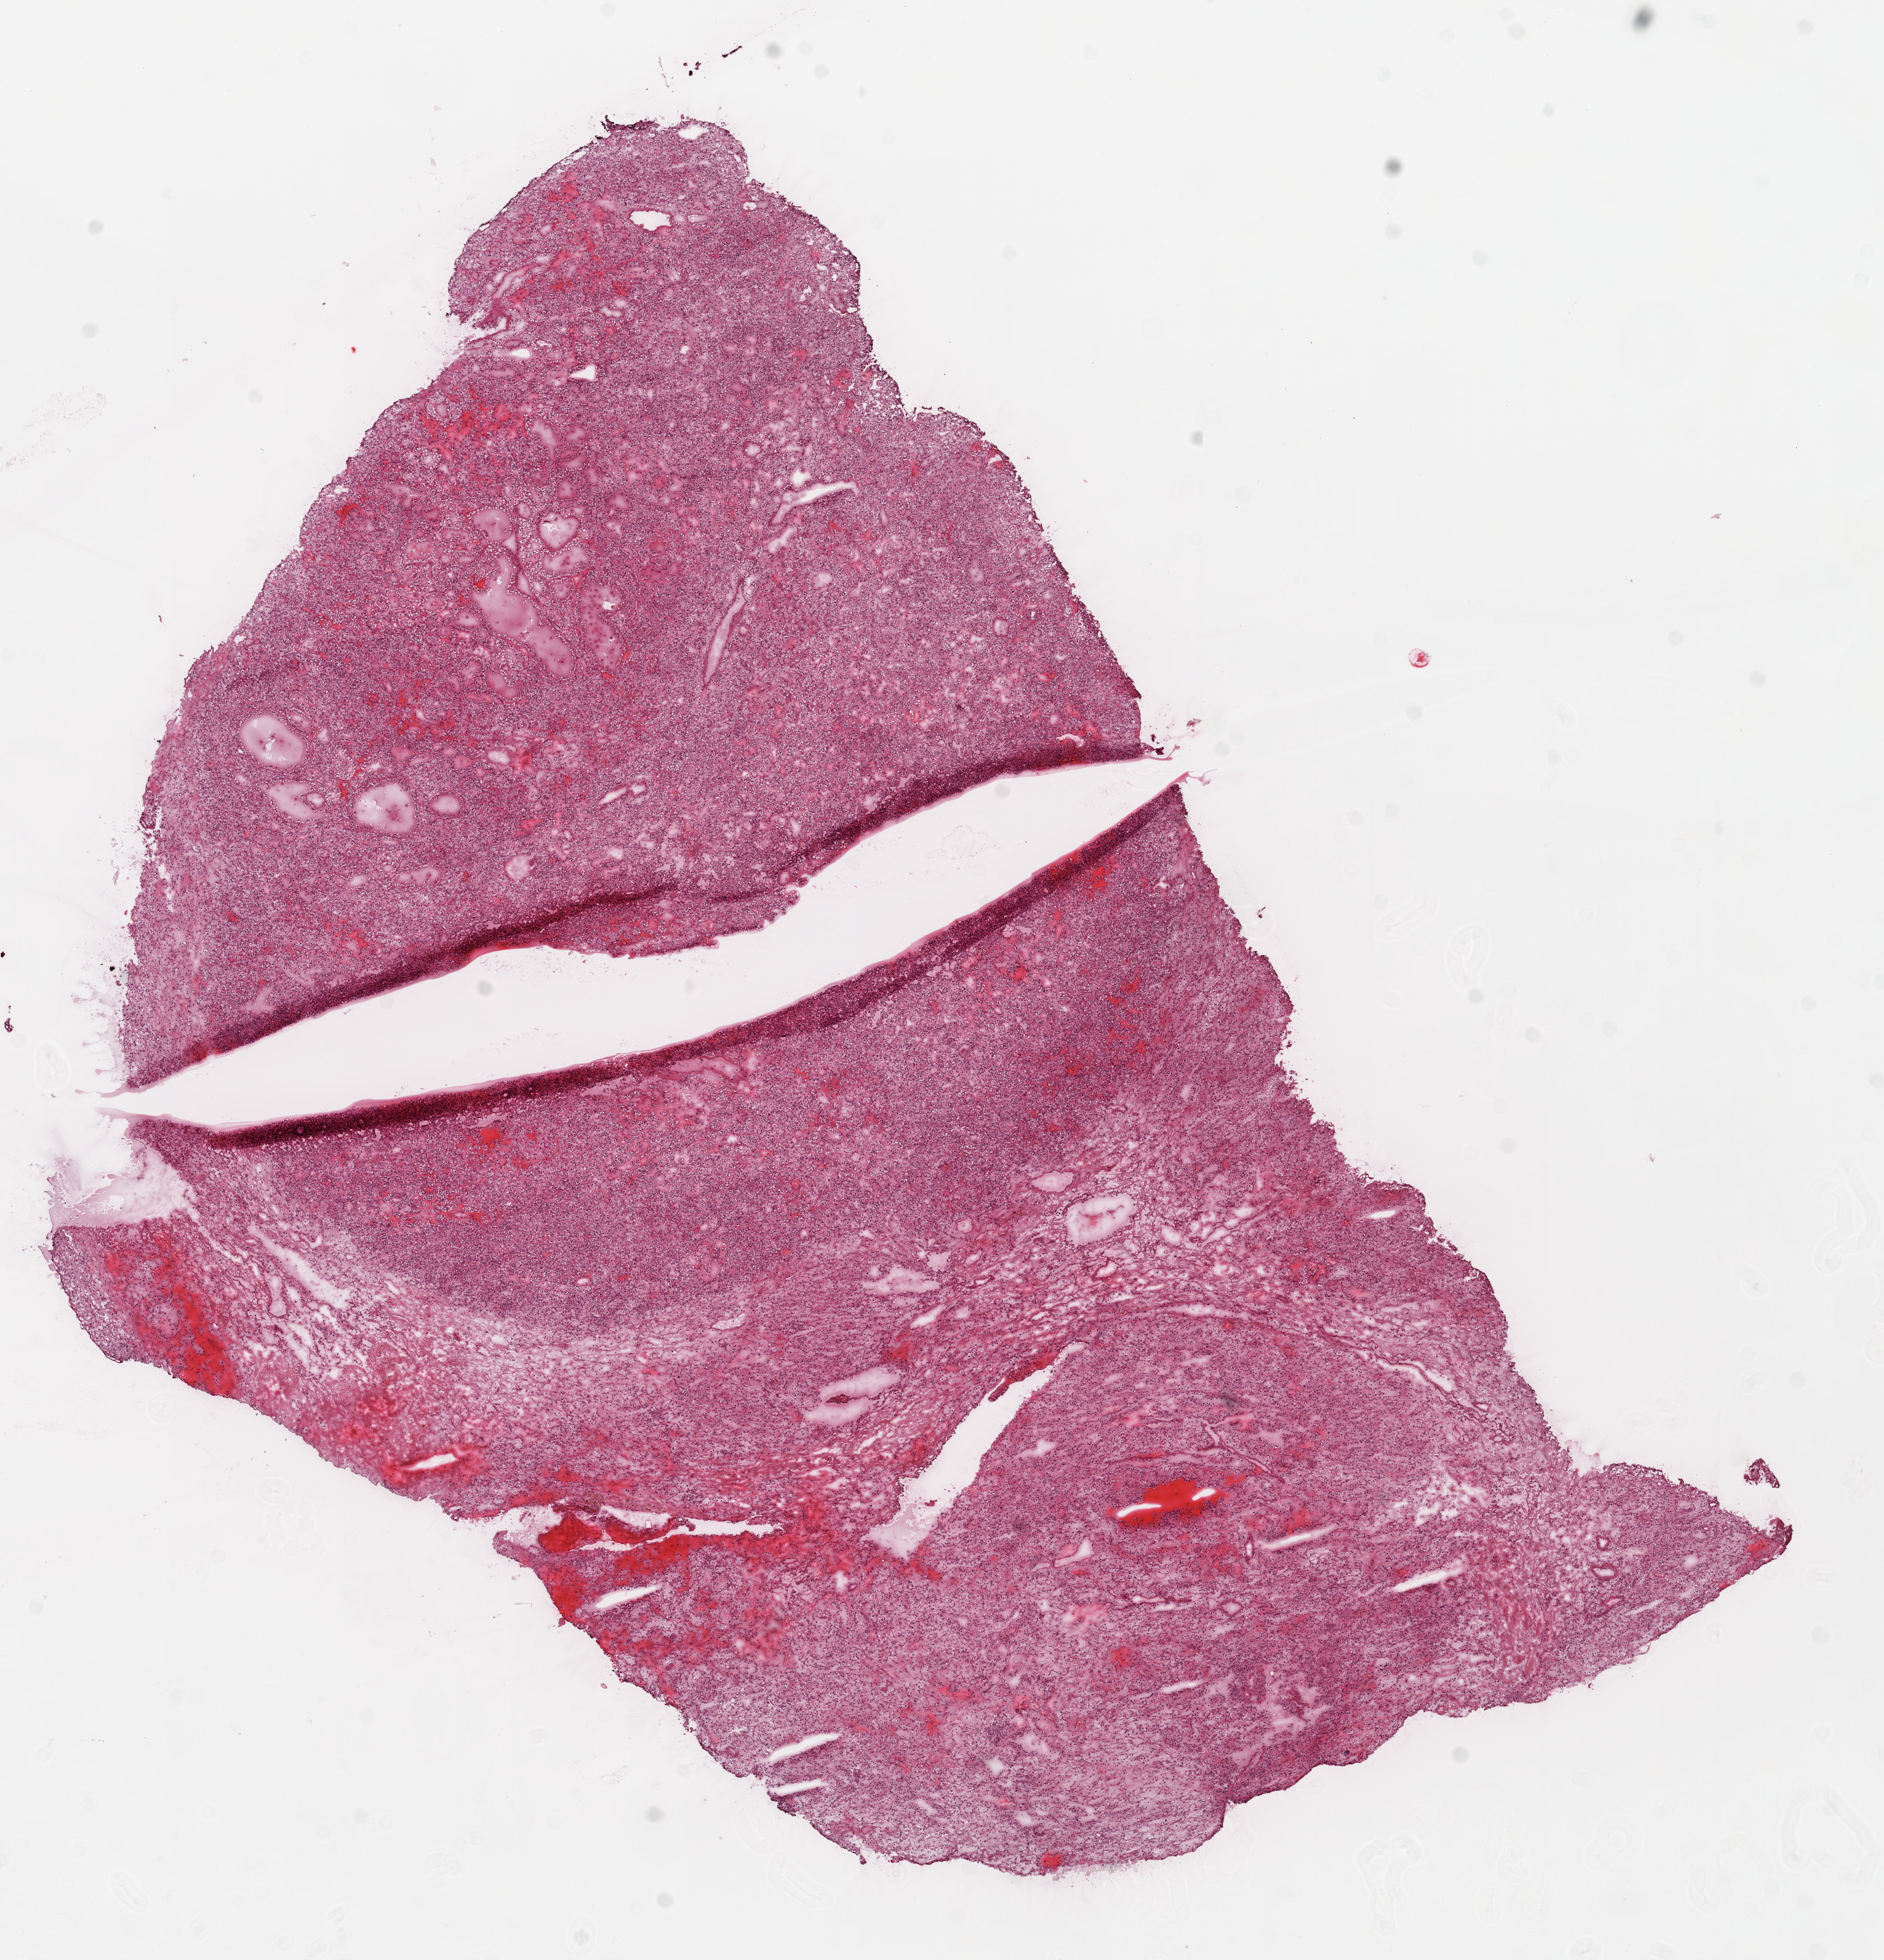
Digitized H&E-stained tissue section (whole slide), a low-resolution overview of the entire scanned area, about 11.0 x 11.5 mm (slide scanned at 20x). Frozen section from the top of the tissue portion. Sample: primary tumour, kidney. Patient: male, age at initial diagnosis 46 years. Histologic grade: G2 (moderately differentiated). Slide review estimates, as recorded: tumour cells 90%, tumour nuclei 80%, normal cells 0%, stromal cells 10%, necrosis 0%.
Histologic diagnosis: Clear cell adenocarcinoma, NOS. AJCC pathologic stage: I.